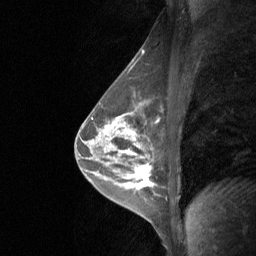
Breast MRI (dynamic contrast-enhanced), one sagittal slice; dynamic contrast-enhanced study with each time point stored as its own series, time point 2 of 3 at this slice position (early post-contrast, ordered by acquisition time); 1.5 T; TE 4.8 ms, TR 27 ms; 2 mm slice thickness; 256 × 256 image matrix. Female patient, age 47 years. Case-level facts recorded for this patient, not image findings: setting: breast cancer imaged before/during neoadjuvant chemotherapy; receptor status: HR-positive, HER2-negative.
Outlined on this slice (semi-automatic segmentation, software-assisted and operator-edited):
- analysis volume of interest (the breast-tissue region the enhancement analysis was run in; not a lesion): bounding box [x1, y1, x2, y2] px = [120, 165, 154, 191]
- tumour enhancement mask (voxels above the 90 % enhancement threshold inside the analysis volume of interest): [138, 169, 148, 184]